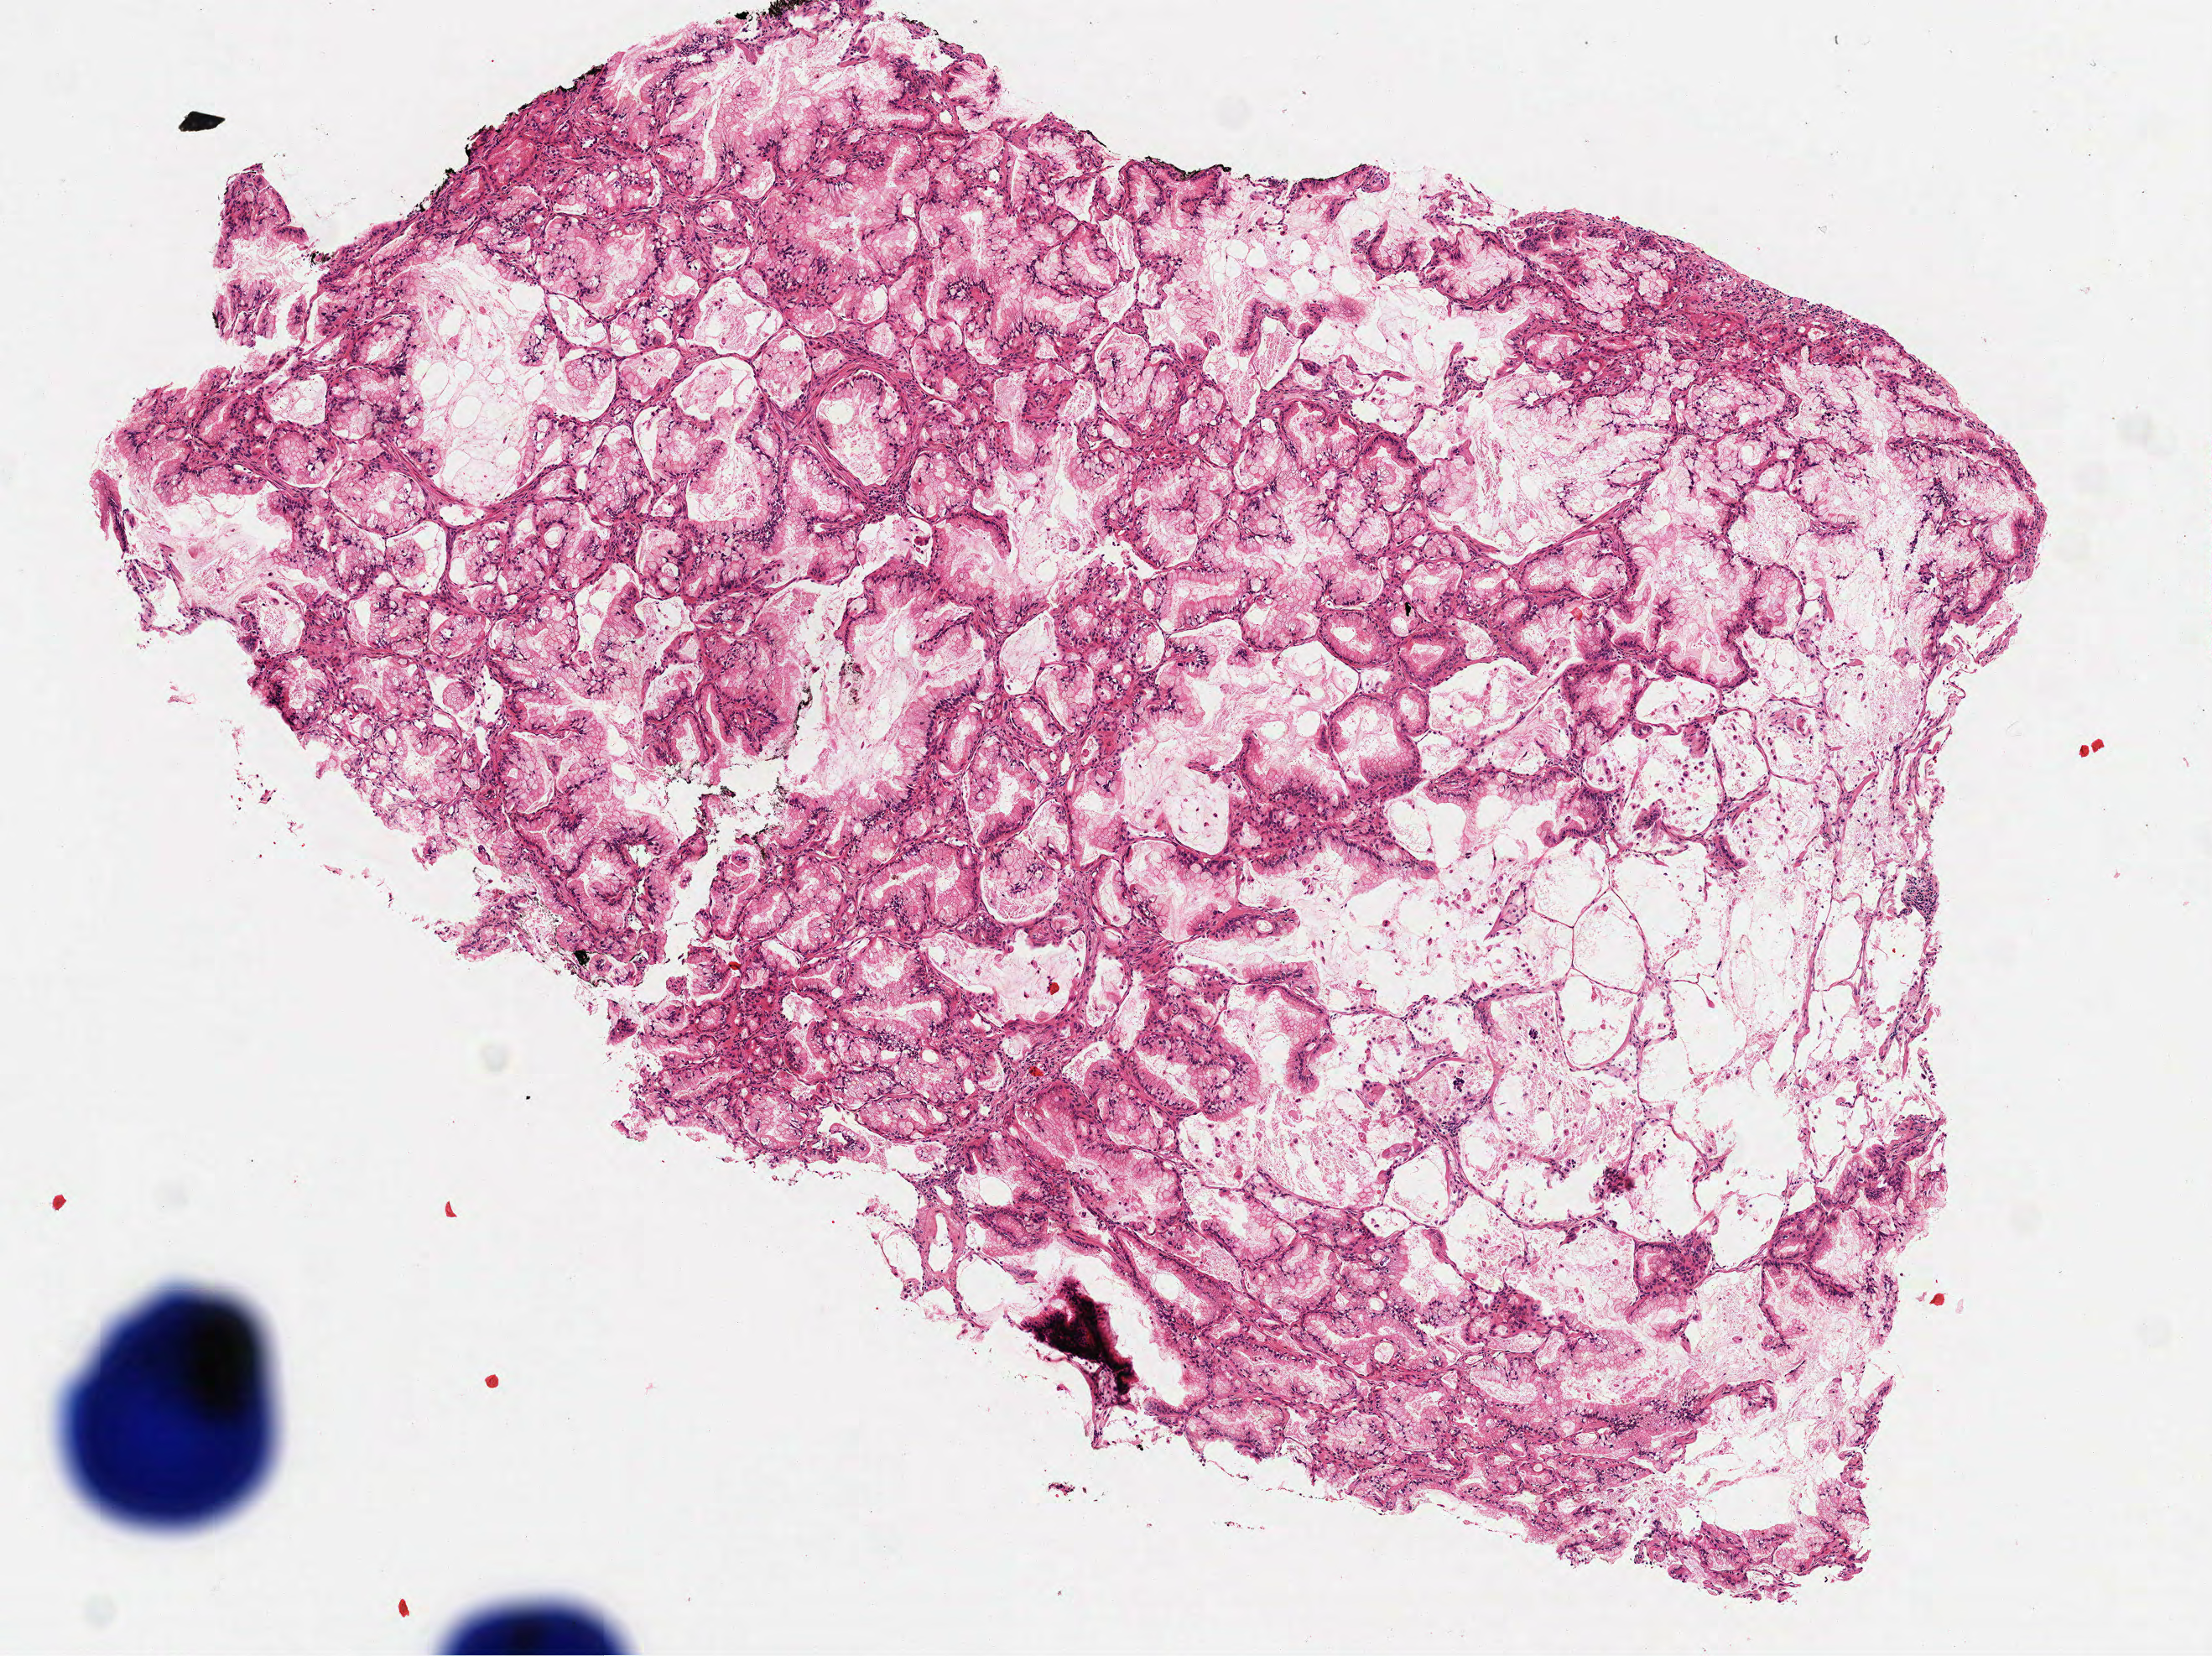
Hematoxylin and eosin (H&E) stained whole-slide image — shown as a low-resolution overview of the whole scanned area (about 5.3 x 4.0 mm, acquisition: 40x scan). Frozen section. Sample: primary tumour, lung. Female patient; age at initial diagnosis 66 years. Slide review estimates, as recorded: tumour cells 100%, tumour nuclei 85%, normal cells 0%, stromal cells 0%, necrosis 0%. Infiltration values recorded for this section: lymphocyte infiltration 1%, monocyte infiltration 1%, neutrophil infiltration 0%.
TNM: T2 N0 M0. Histologic diagnosis: Bronchio-alveolar carcinoma, mucinous (lower lobe, lung). AJCC pathologic stage: IB (6th edition).